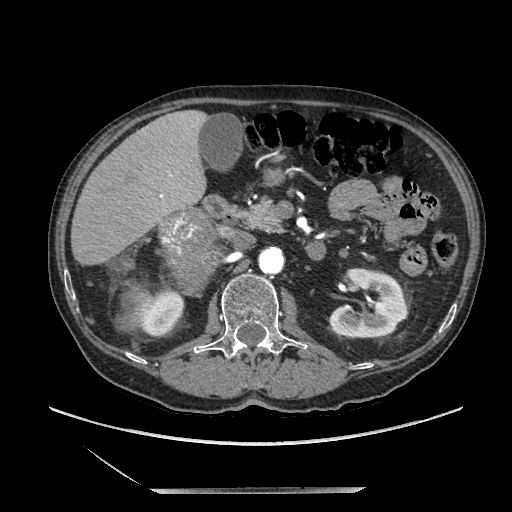
Contrast-enhanced abdominal CT, one axial slice; position 99 of 243 along the scan axis; soft-tissue window (W 400 / L 40 HU); 1.25 mm slice thickness; 512 × 512 image matrix. Male patient. Case-level facts recorded for this patient, not image findings: diagnosis: adrenocortical carcinoma; tumour side: right adrenal; tumour size at pathology: 16 cm.
Annotated regions visible in this slice (semi-automatic segmentation, software-assisted and operator-edited):
- mass: bounding box [x1, y1, x2, y2] px = [161, 211, 215, 289]